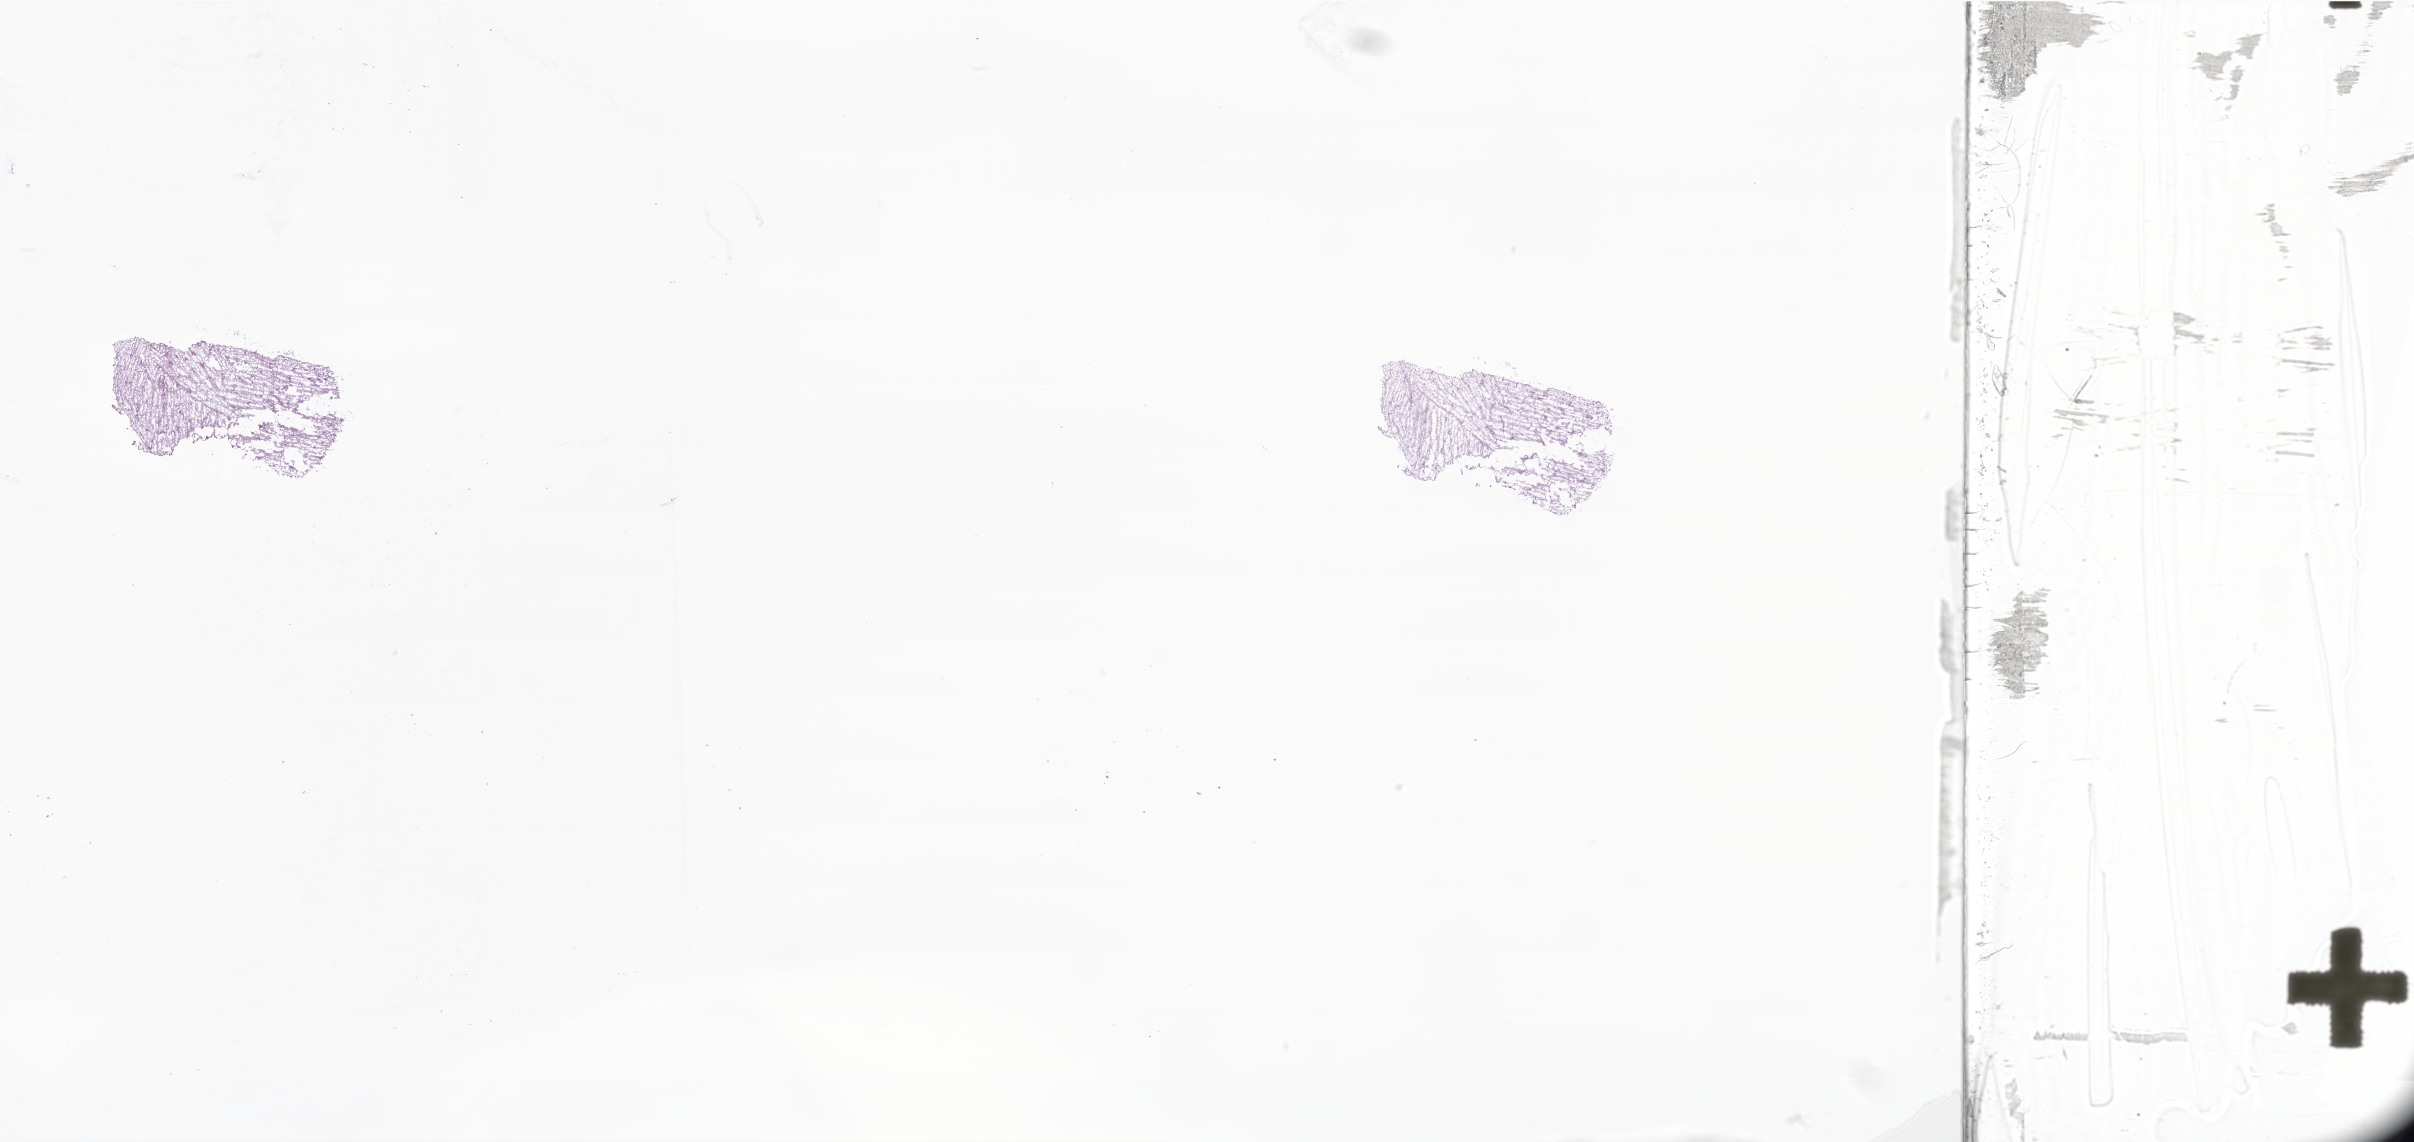
Whole-slide image, hematoxylin and eosin (H&E) stain of tumor tissue from the brain, shown as a low-resolution overview of the whole scanned area (about 40.4 x 19.1 mm). Frozen section (OCT-embedded). Patient male; age 79 months (6 years 7 months).
Diagnosis: Neoplasm, uncertain whether benign or malignant.